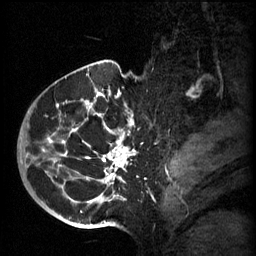
Breast MRI (dynamic contrast-enhanced), one sagittal slice; position 44 of 60 along the scan axis; 3 images stored at this slice position (order not interpretable as contrast timing); 1.5 T; TE 4.2 ms, TR 11 ms; 2 mm slice thickness; 256 × 256 image matrix. Patient: female, 51 years.
Structures marked on this image (semi-automatically segmented with operator editing):
- analysis volume of interest (the breast-tissue region the enhancement analysis was run in; not a lesion): bounding box (x1, y1, x2, y2) in pixels: (48, 82, 155, 197)
- tumour enhancement mask (voxels above the 70 % enhancement threshold inside the analysis volume of interest): (48, 90, 136, 197)